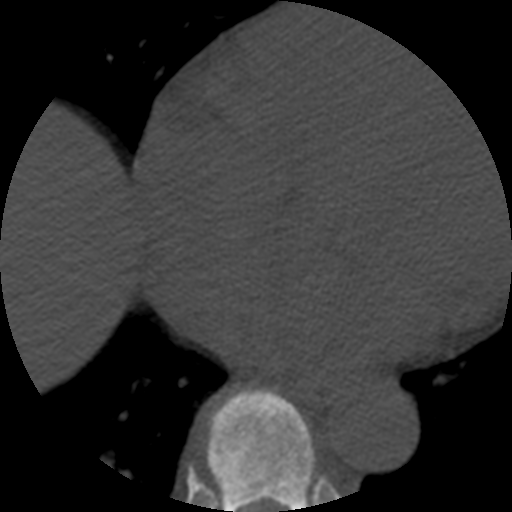
CT including the spine, one axial slice; slice 319 of 508 in the series (ordered by position); reconstruction kernel STANDARD; bone window (W 1800 / L 400 HU); 1.25 mm slice thickness; 512 × 512 image matrix. Patient age 57 years. From the clinical record (not read from this slice): primary cancer: prostate.
Structures marked on this image (semi-automatically segmented with operator editing):
- T8 vertebra: bounding box <207,389,316,512> (left, top, right, bottom; pixels)